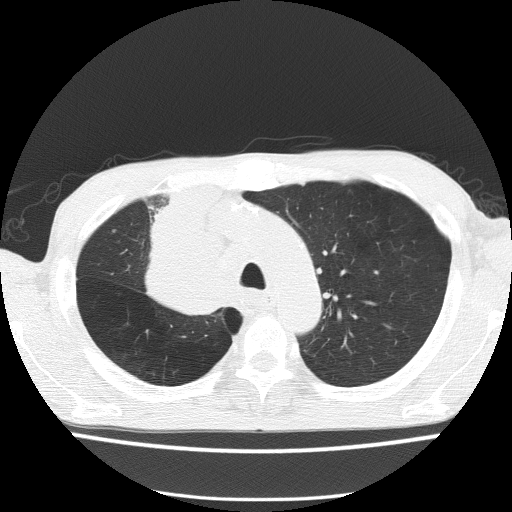
Low-dose screening chest CT, one axial slice; slice 112 of 150 in the series (ordered by position); reconstruction kernel FC51; lung window (W 1500 / L -600 HU); 2 mm slice thickness; 512 × 512 image matrix, field of view 336 × 336 mm.
Outlined on this slice (manually delineated by an expert):
- lesion 1 (tumor, hilum of right lung): bounding box [x1, y1, x2, y2] px = [146, 187, 220, 315]